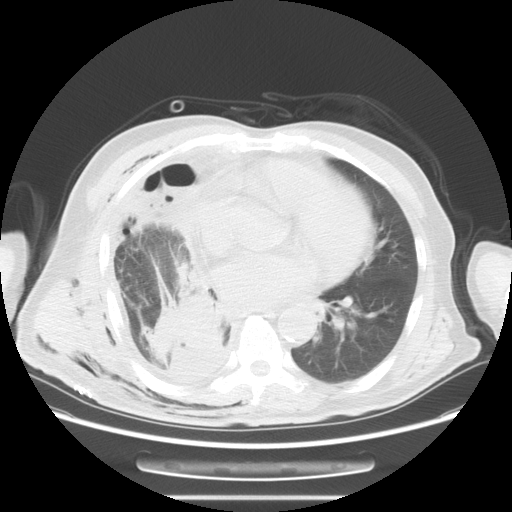
Chest CT, one axial slice; position 29 of 59 along the scan axis; 120 kVp; lung window (W 1500 / L -600 HU); 512 × 512 image matrix. Patient: male, 69 years. From the clinical record (not read from this slice): clinical TNM (as recorded): T3 N0 M0; histopathological grade: G2-3.
Annotated regions visible in this slice (bounding box drawn by a radiologist):
- lung tumour (recorded histology: squamous cell carcinoma): bounding box <141,287,232,385> (left, top, right, bottom; pixels)